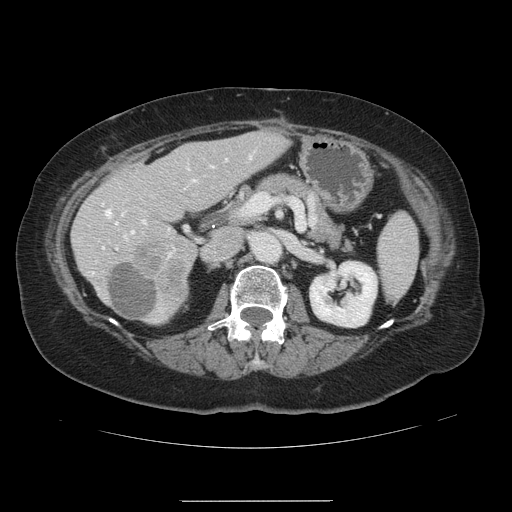
Contrast-enhanced abdominal CT, one axial slice; slice 61 of 141 in the series (ordered by position); intravenous contrast given; soft-tissue window (W 400 / L 40 HU); 512 × 512 image matrix. Female patient, age 74 years. From the clinical record (not read from this slice): diagnosis: colorectal cancer liver metastases, imaged before liver resection; multiple liver metastases: yes; largest metastasis: 7 cm; chemotherapy before resection: no.
Structures marked on this image (expert manual segmentation):
- hepatic veins: bounding box [x1, y1, x2, y2] px = [105, 210, 135, 235]
- liver: [72, 132, 288, 325]
- planned liver remnant (the part of the liver to remain after resection): [74, 132, 288, 322]
- portal vein (with intrahepatic branches): [115, 156, 251, 256]
- liver metastasis: [109, 264, 158, 320]
- liver metastasis: [130, 242, 190, 295]